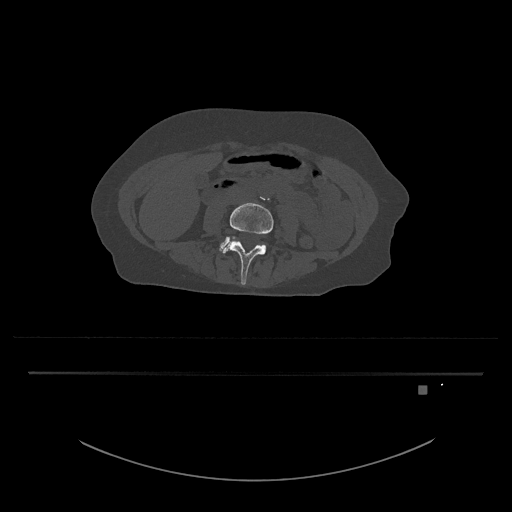
CT including the spine, one axial slice; position 356 of 797 along the scan axis; reconstruction kernel Br40s/3; 120 kVp; bone window (W 1800 / L 400 HU); 0.5 mm slice thickness; 512 × 512 image matrix, field of view 500 × 500 mm. Female patient, age 57 years. Case-level facts recorded for this patient, not image findings: primary cancer: cervical.
Structures marked on this image (semi-automatic segmentation, software-assisted and operator-edited):
- L4 vertebra: box from (x=221, y=202) to (x=274, y=285) px